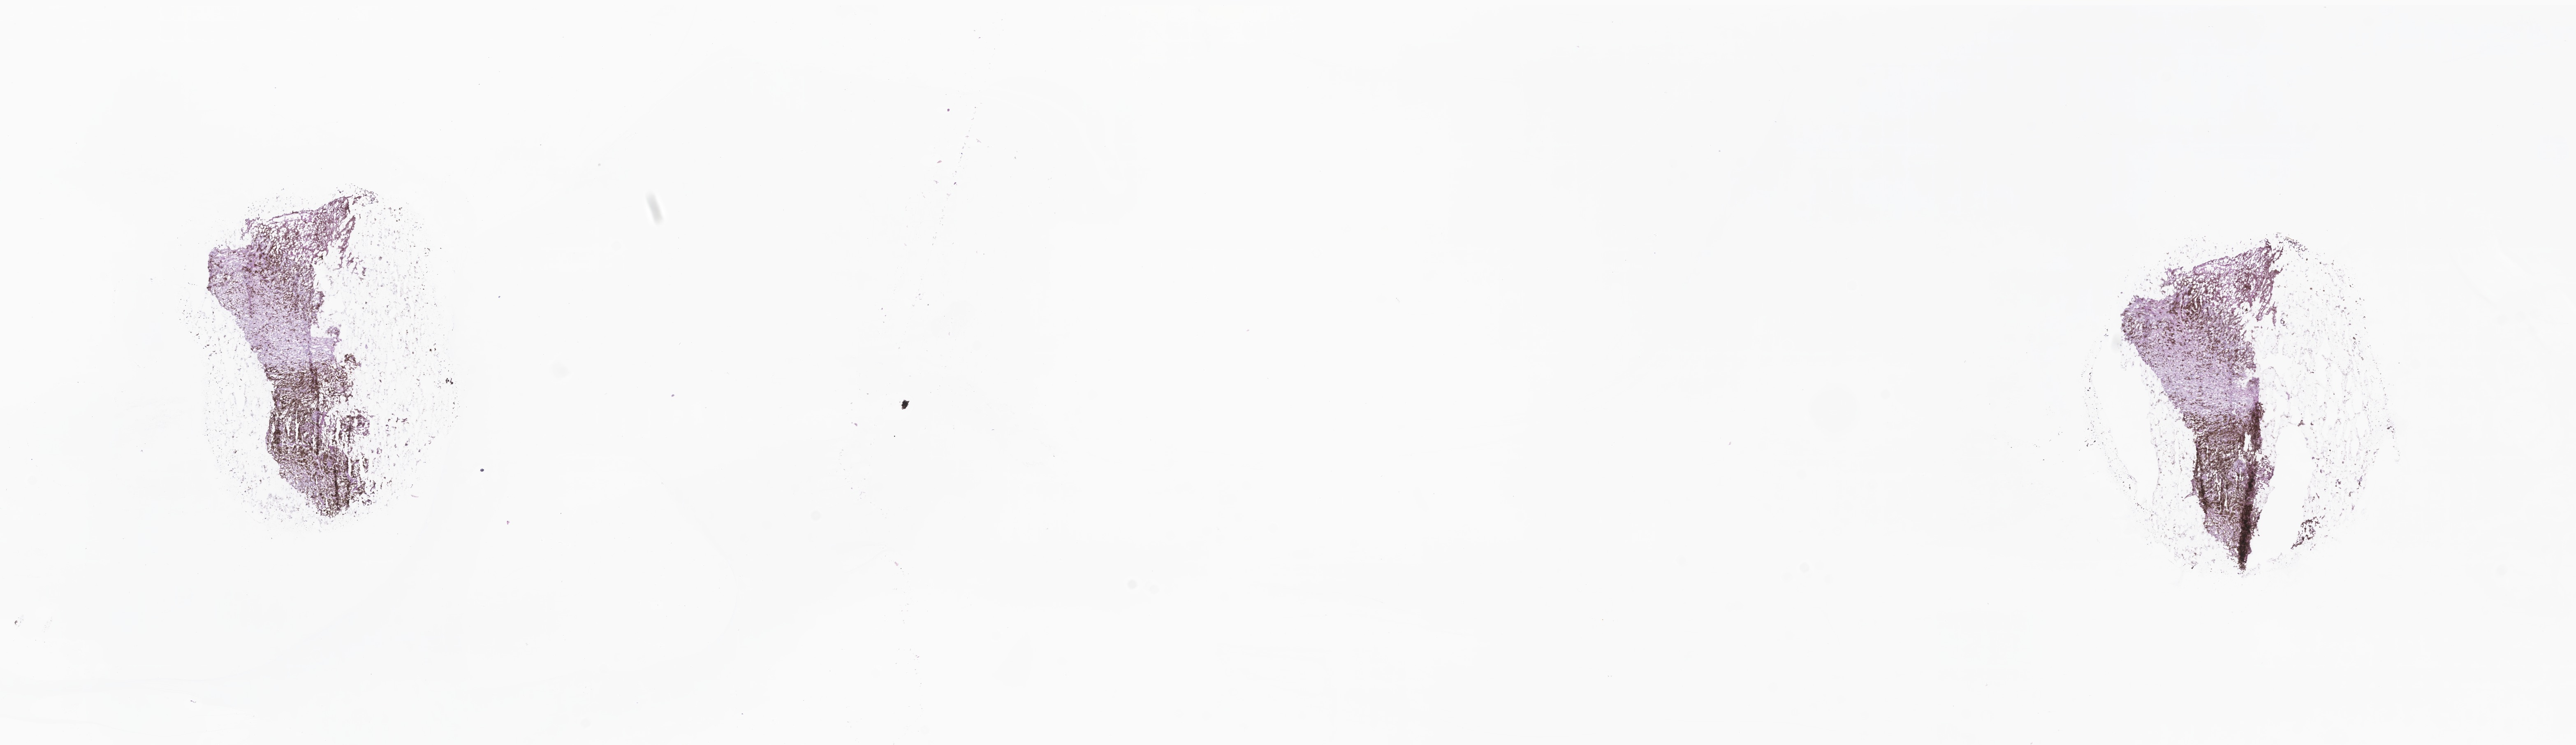
Hematoxylin and eosin (H&E) whole-slide image — shown as a low-resolution overview of the whole scanned area (about 26.4 x 7.6 mm). Cryosection. Specimen: metastatic tumor tissue, resected from lymph node. Female patient; age at initial diagnosis 70 years. Slide review estimates, as recorded: tumor cells 70%, tumor nuclei 90%, stromal cells 20%, necrosis 10%, normal cells 0%. Inflammatory infiltration, as recorded: lymphocyte infiltration 0%, monocyte infiltration 0%, neutrophil infiltration 0%.
- patient diagnosis (primary): Malignant melanoma, NOS